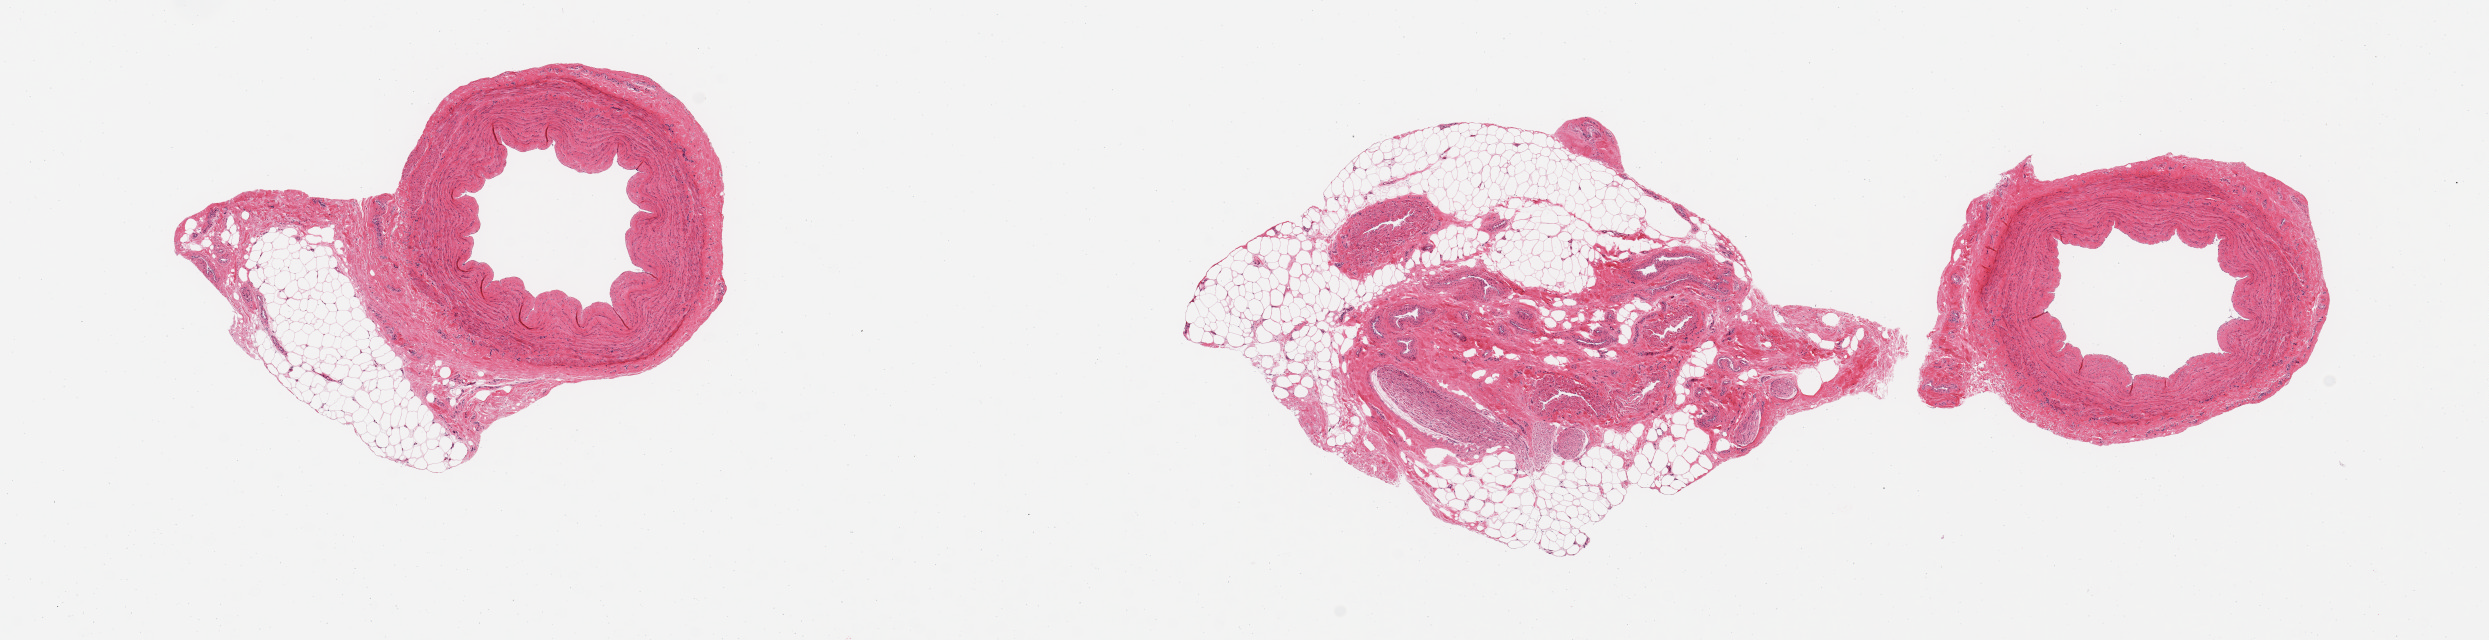
Digitized haematoxylin and eosin-stained section, shown as a low-resolution overview of the whole scanned area (about 19.7 x 5.1 mm); PAXgene-fixed, paraffin-embedded tissue; section of tibial artery (target tissue); donor tissue sample. Donor: male.
- pathologist's review note for this sample: 2 pieces, no atherosis; Beware ~6mm extraneous fragments of fat/fibroadipose tissue present in section